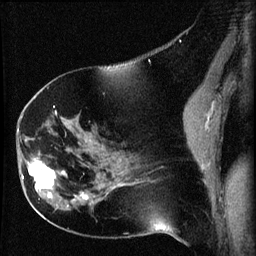
Breast MRI (dynamic contrast-enhanced), one sagittal slice. Slice 31 of 60 in the series (ordered by position). Dynamic contrast-enhanced series, image 2 of 3 at this slice position (ordered by acquisition). 1.5 T. TE 4.2 ms, TR 8.2 ms. 2 mm slice thickness. 256 × 256 image matrix, field of view 180 × 180 mm. Patient: female, 63 years.
Annotated regions visible in this slice (semi-automatic segmentation, software-assisted and operator-edited):
- analysis volume of interest (the breast-tissue region the enhancement analysis was run in; not a lesion): bounding box [x1, y1, x2, y2] px = [22, 156, 64, 202]
- tumour enhancement mask (voxels above the 70 % enhancement threshold inside the analysis volume of interest): [22, 158, 64, 197]